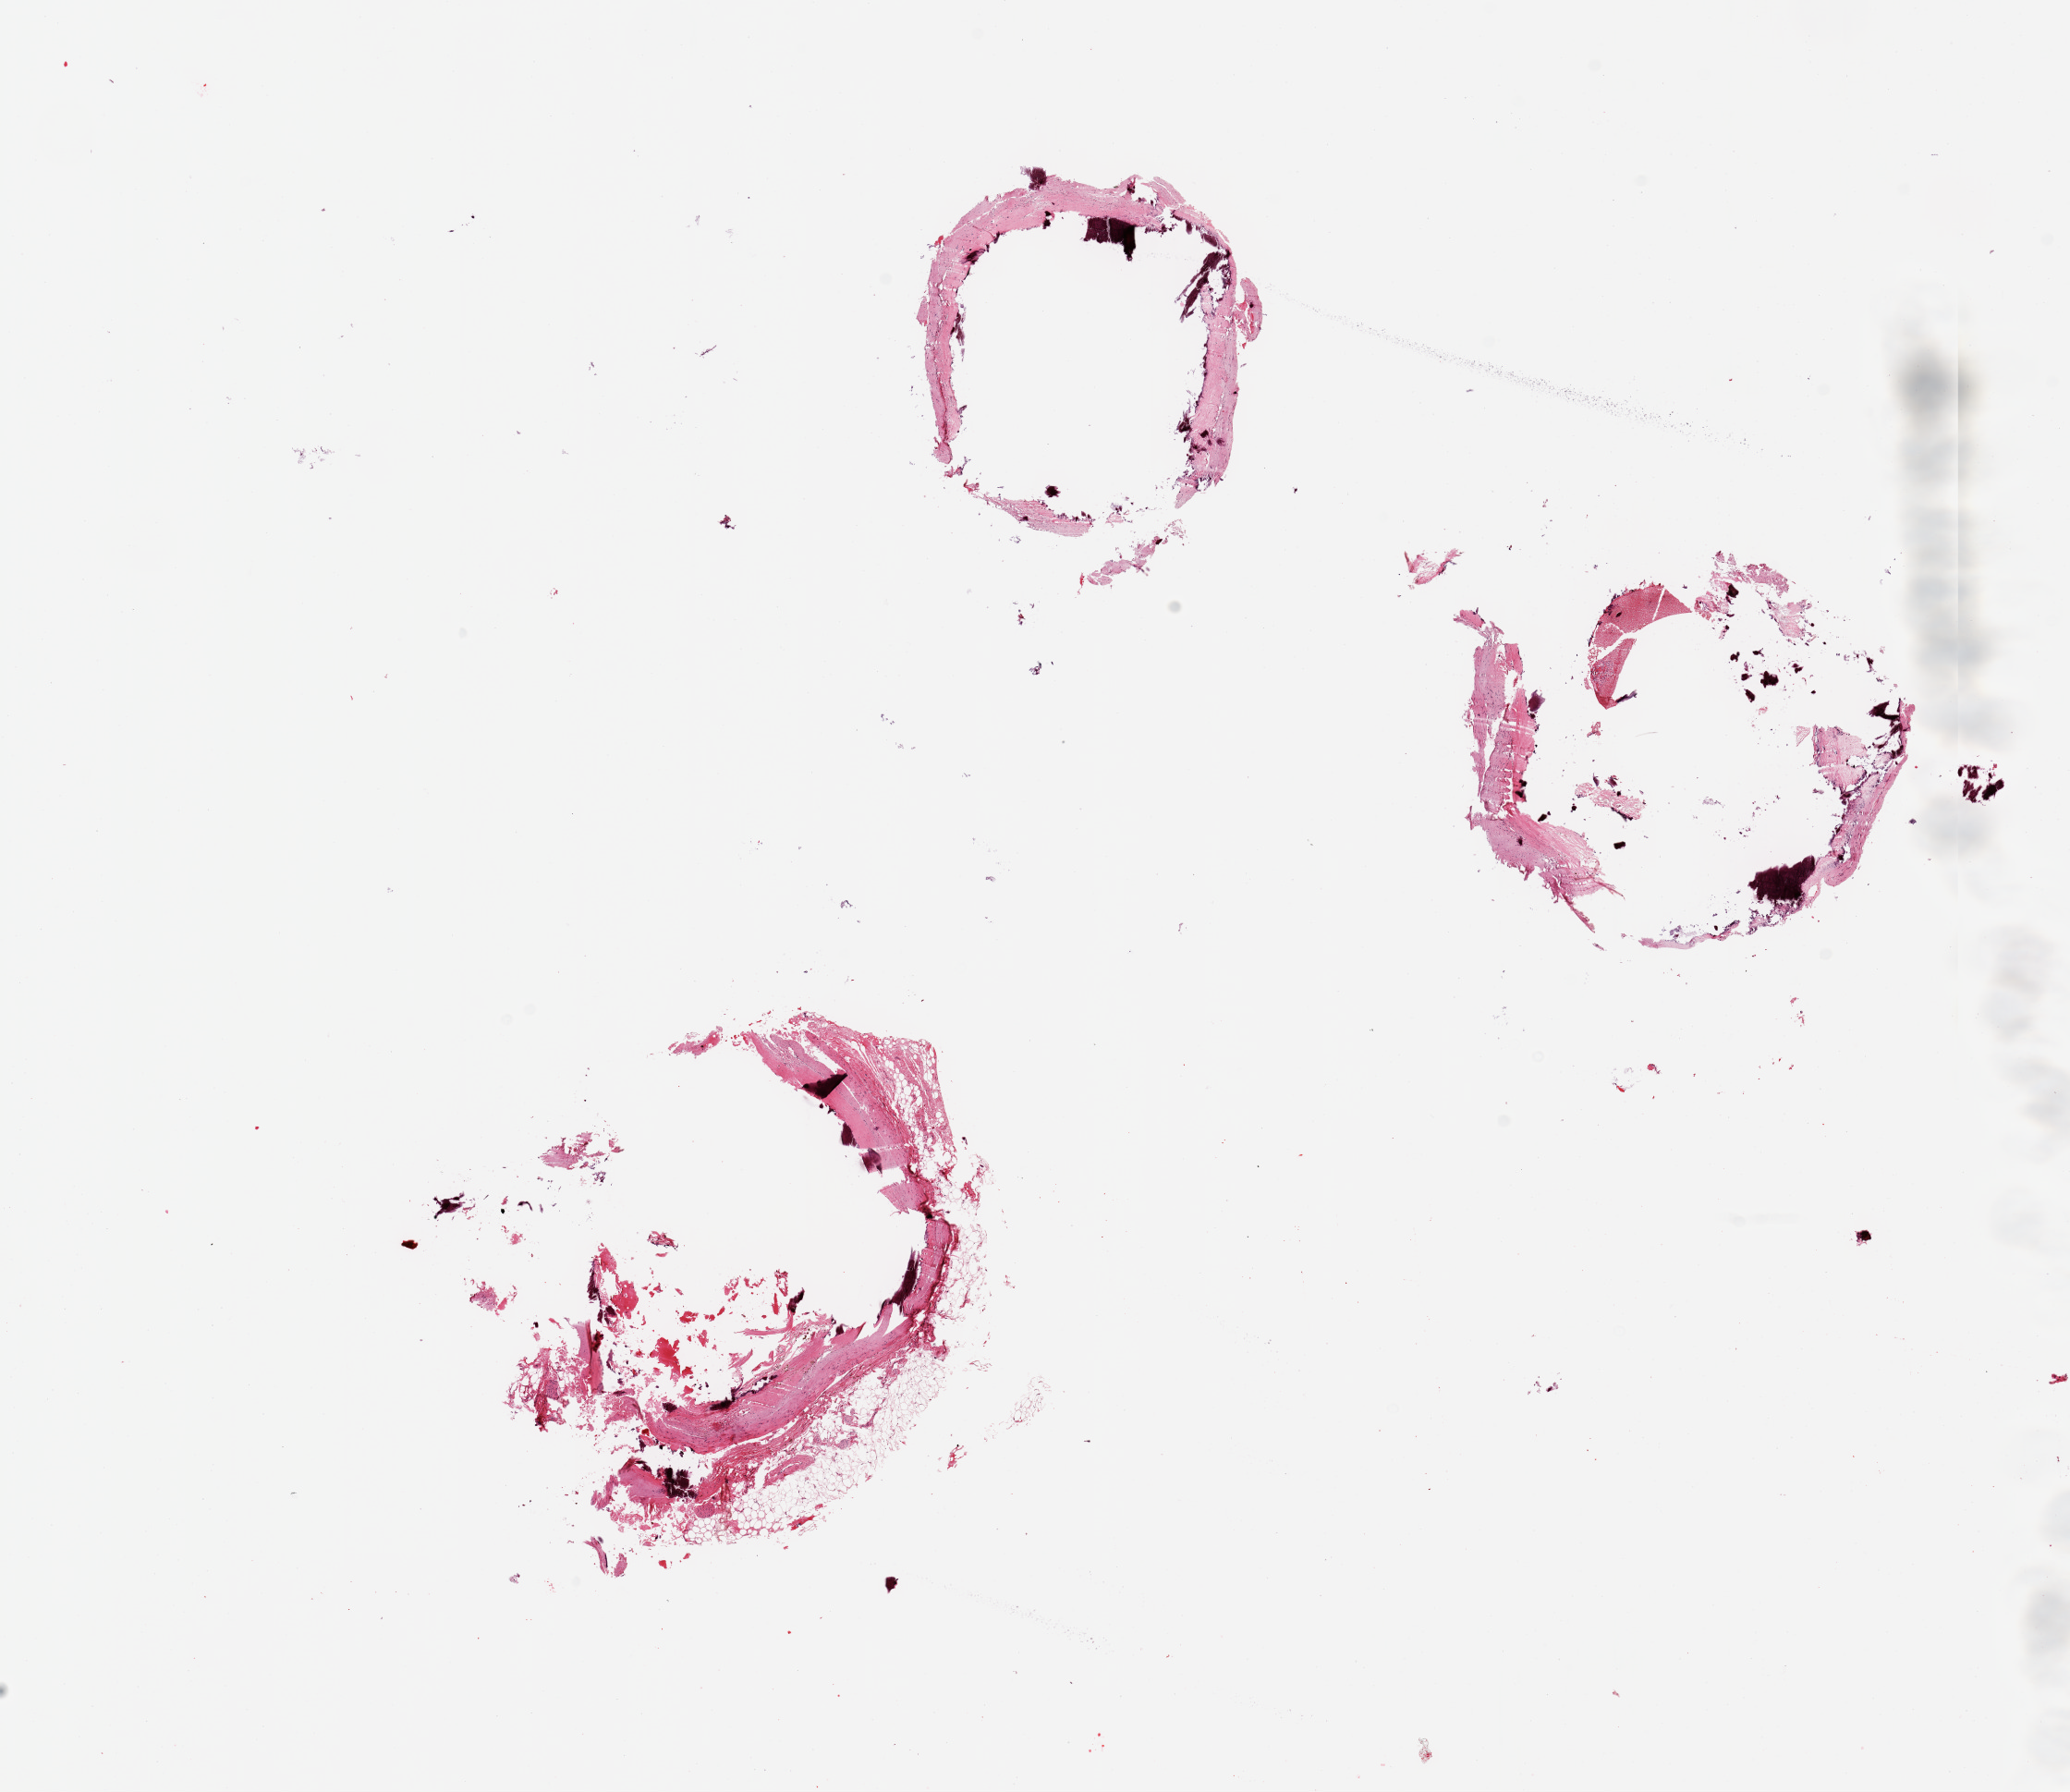
H&E whole-slide image — a low-resolution overview of the entire scanned area, about 17.7 x 15.3 mm. PAXgene-fixed, paraffin-embedded tissue. Target tissue: coronary artery. Donor tissue sample. Donor sex: male.
Review note (as recorded): 3 pieces; calcified, sclerotic, fragmented; no normal tissue remains; [had coronary bypass].